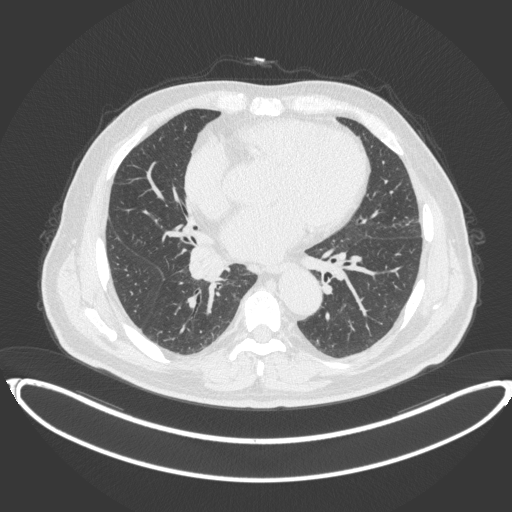
Chest CT, one axial slice; position 189 of 383 along the scan axis; reconstruction kernel B31f; 120 kVp; lung window (W 1500 / L -600 HU); 1 mm slice thickness; 512 × 512 image matrix, field of view 448 × 448 mm. Male patient, age 61 years. From the clinical record (not read from this slice): clinical TNM (as recorded): T1b N1 M0.
Annotated regions visible in this slice (rectangle marked by the reading radiologist):
- lung tumour (recorded histology: squamous cell carcinoma): bounding box <186,239,232,284> (left, top, right, bottom; pixels)